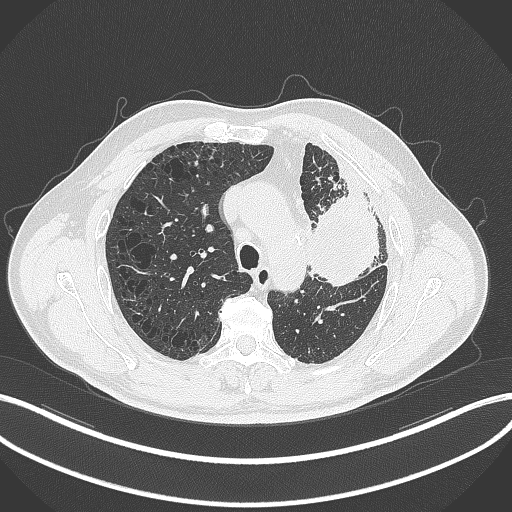
Chest CT, one axial slice; position 225 of 297 along the scan axis; 120 kVp; lung window (W 1500 / L -600 HU); 512 × 512 image matrix, field of view 400 × 400 mm. Patient: male, 68 years. Case-level facts recorded for this patient, not image findings: clinical TNM (as recorded): T3 N3 M1.
Annotated regions visible in this slice (rectangle marked by the reading radiologist):
- lung tumour (recorded histology: adenocarcinoma): box from (x=311, y=175) to (x=382, y=295) px